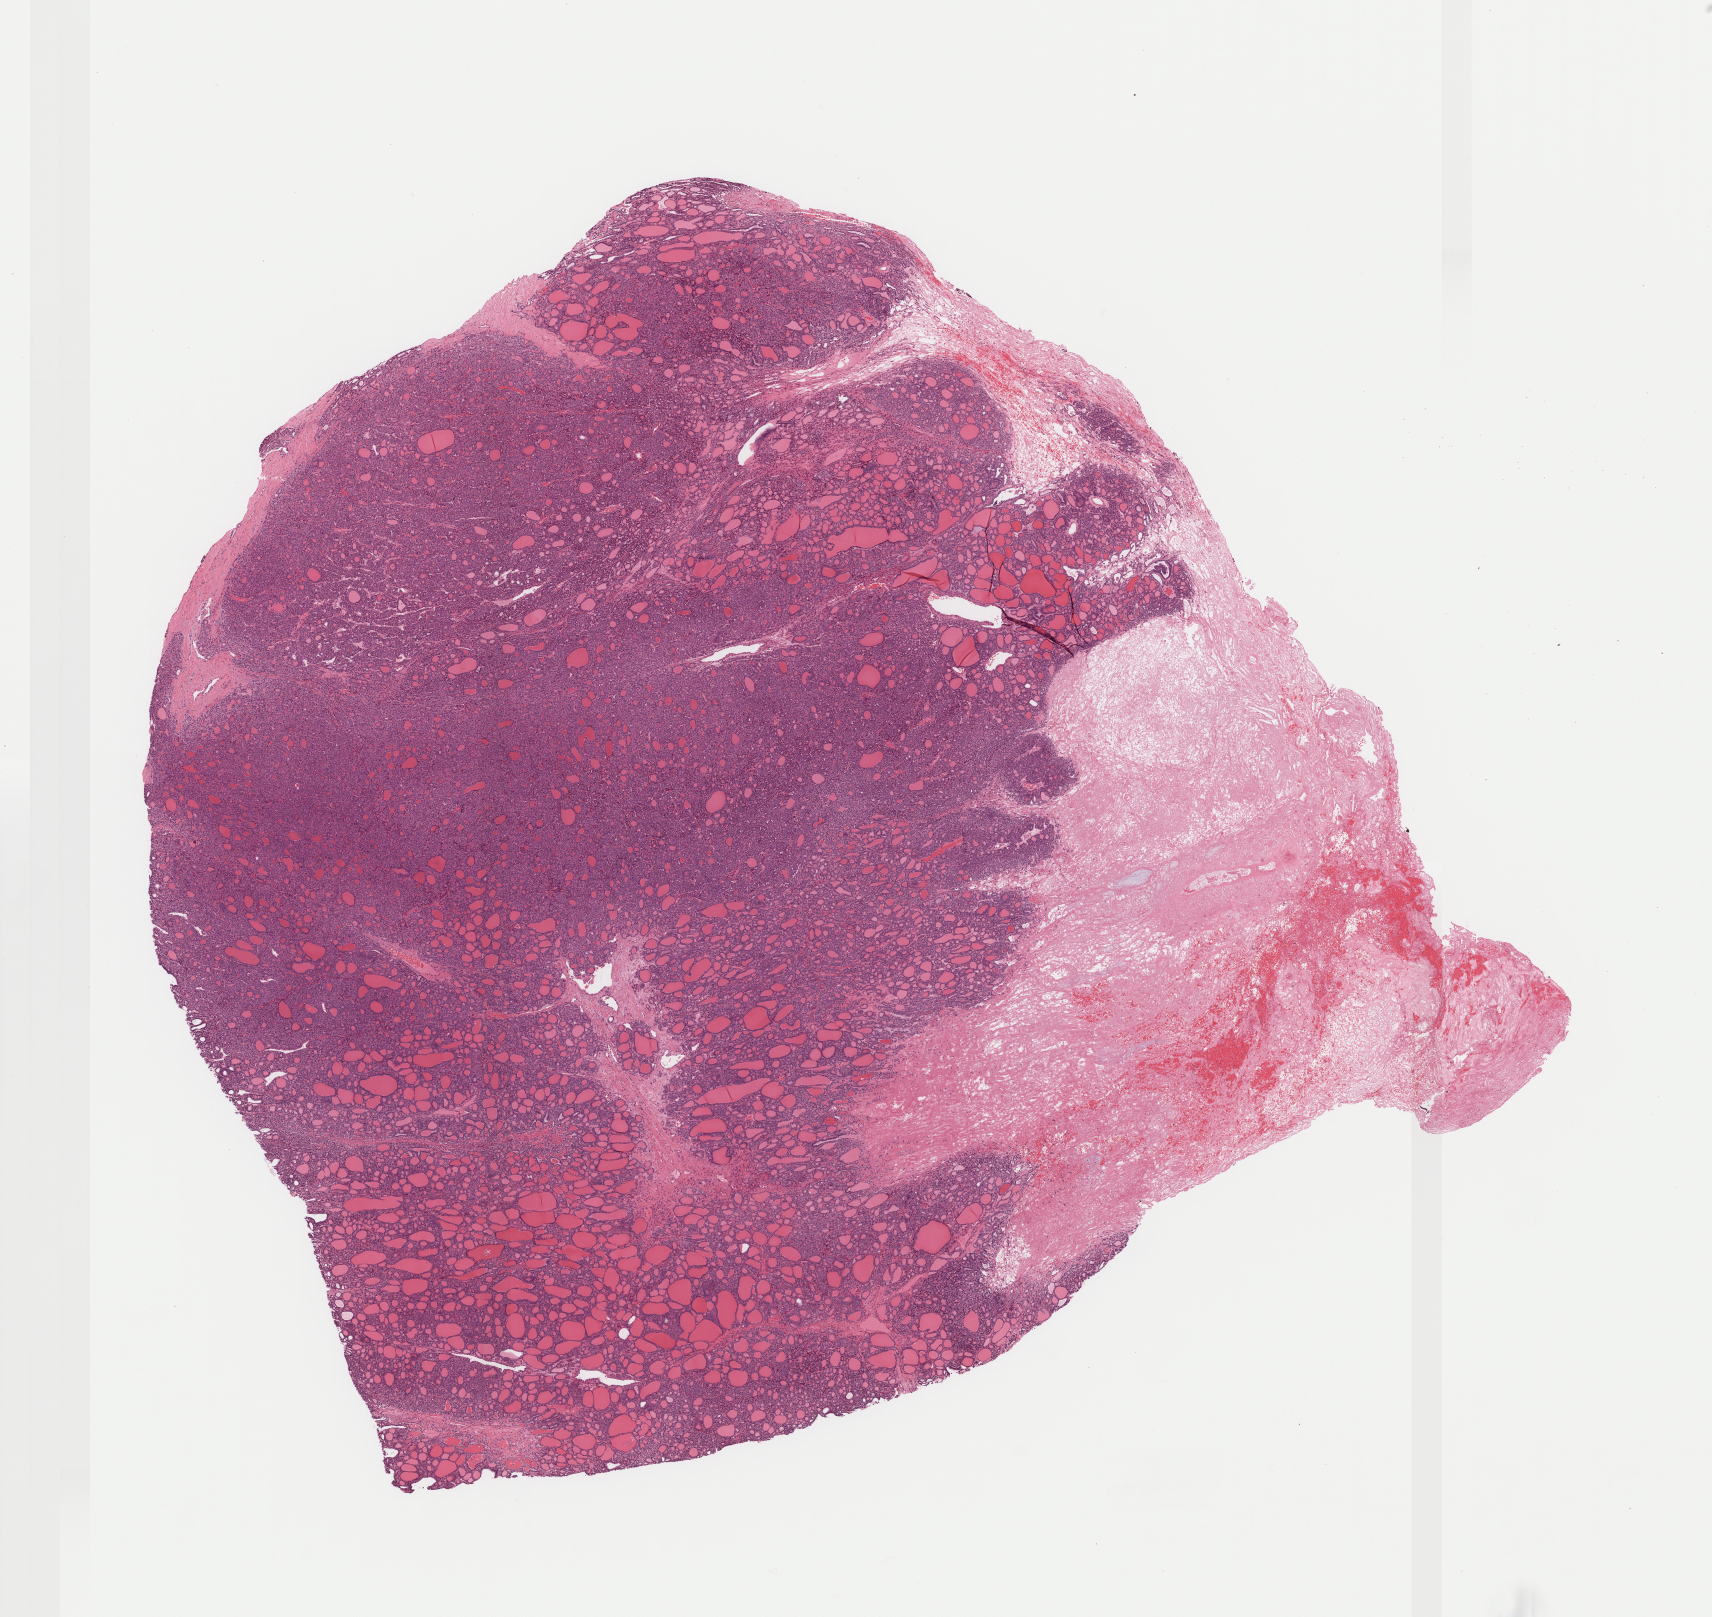
Hematoxylin and eosin (H&E) stained whole-slide image — low-resolution overview of the scanned area, about 13.8 x 13.0 mm (acquisition: 40x scan). FFPE section. Primary tumour sample from the thyroid. Male, age 62 years at initial diagnosis.
Histologic diagnosis: Papillary carcinoma, follicular variant (thyroid gland).